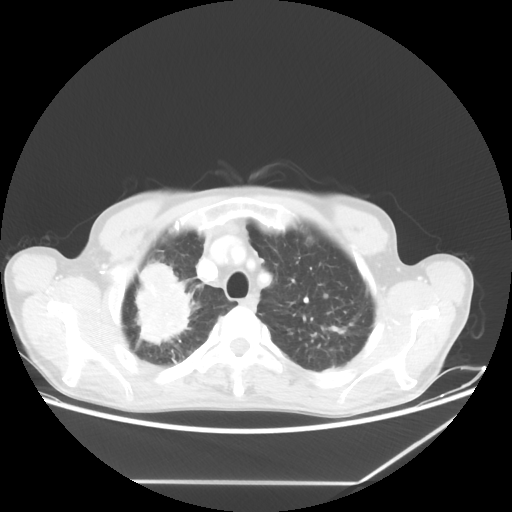
Chest CT, one axial slice; slice 53 of 65 in the series (ordered by position); 80 kVp; lung window (W 1500 / L -600 HU); 5 mm slice thickness; 512 × 512 image matrix. Patient: male, 68 years. Case-level facts recorded for this patient, not image findings: clinical TNM (as recorded): T3 N3 M0.
Outlined on this slice (bounding box drawn by a radiologist):
- lung tumour (recorded histology: adenocarcinoma): box from (x=121, y=262) to (x=198, y=357) px